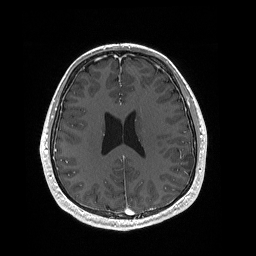
Brain MRI from a brain-tumour surgery series, one axial slice. T1-weighted post-contrast. 256 × 256 image matrix. From the clinical record (not read from this slice): histopathology: Dysembryoplastic neuroepithelial tumor; WHO grade: 1; IDH mutation: no; tumour location: Left Inferior Parietal.
Outlined on this slice (outlined manually by an expert reader):
- tumour: bounding box <180,160,189,166> (left, top, right, bottom; pixels)